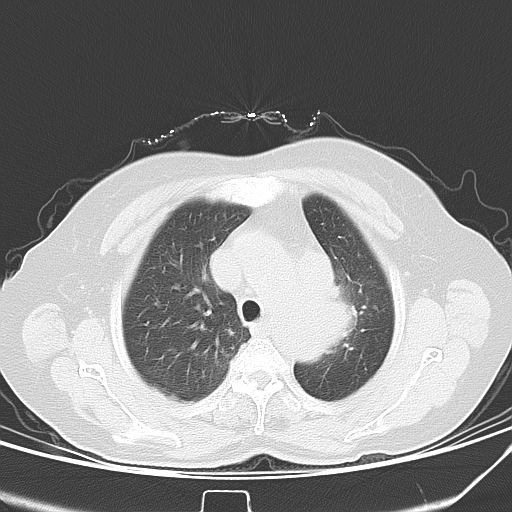
Chest CT, one axial slice. Position 32 of 40 along the scan axis. 120 kVp. Lung window (W 1500 / L -600 HU). 5 mm slice thickness. 512 × 512 image matrix. Female patient, age 59 years. Case-level facts recorded for this patient, not image findings: clinical TNM (as recorded): T3 N1 M0.
Structures marked on this image (rectangle marked by the reading radiologist):
- lung tumour (recorded histology: small cell carcinoma): bounding box [x1, y1, x2, y2] px = [331, 280, 362, 352]